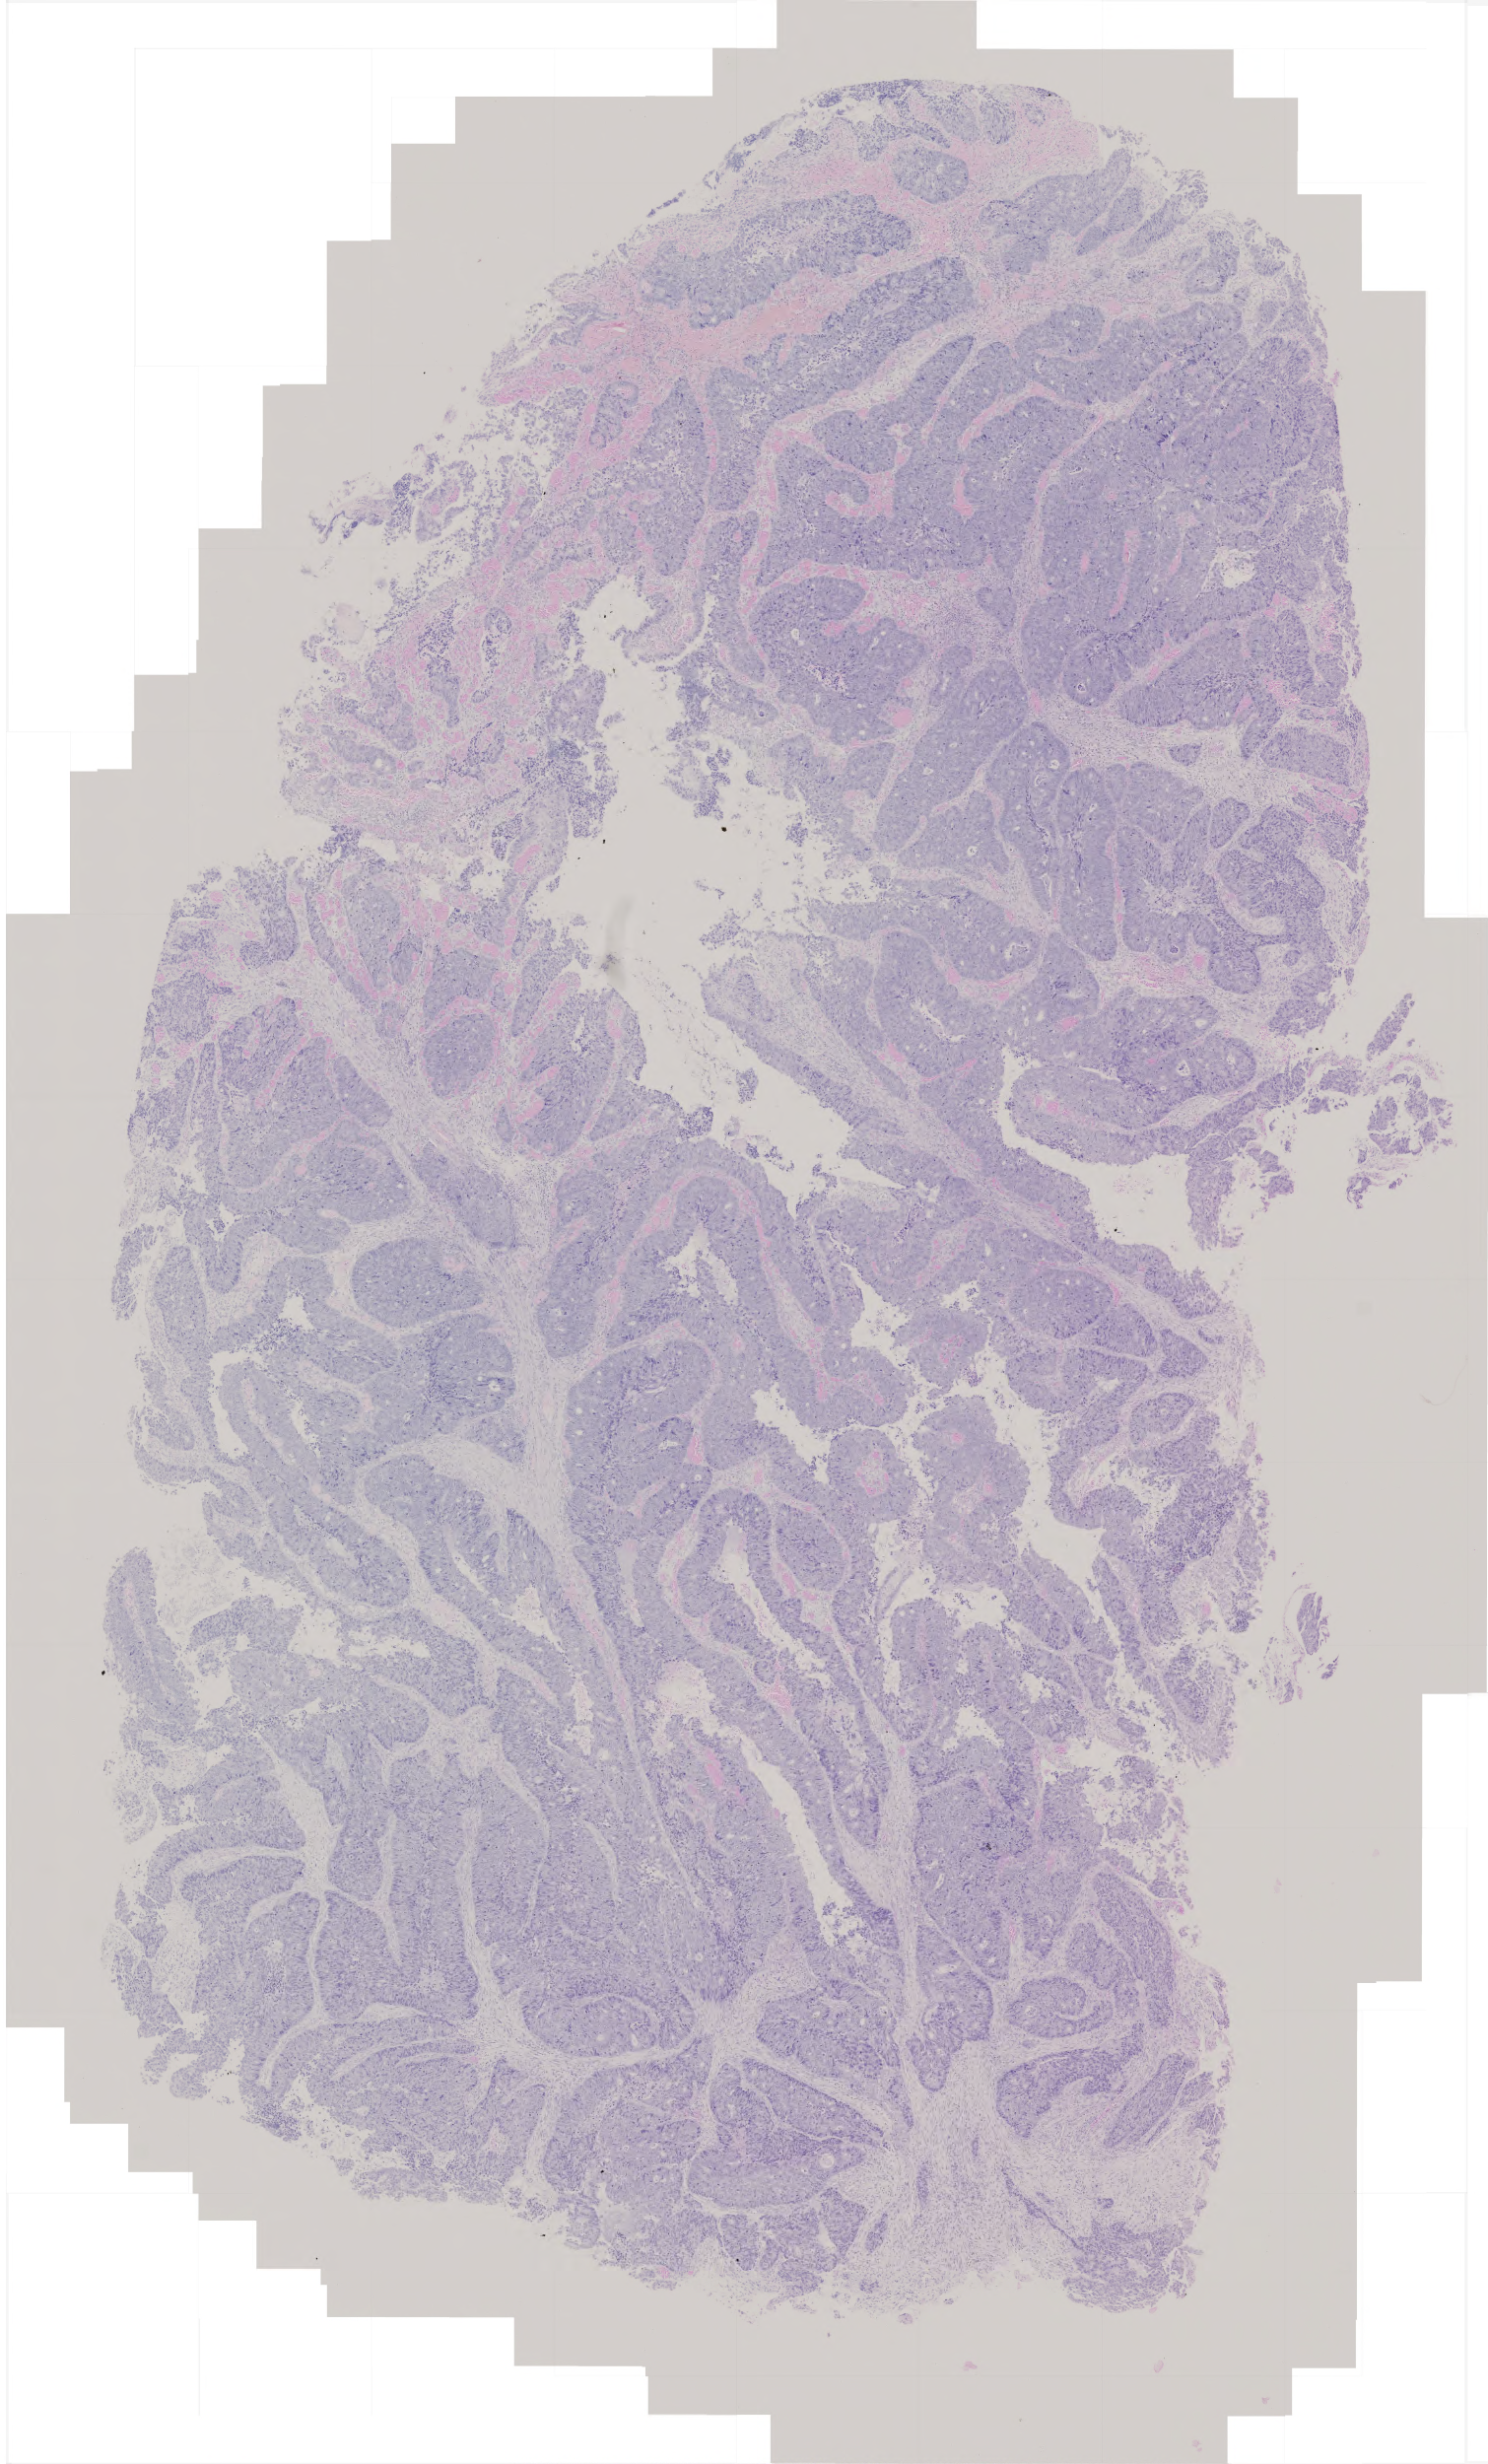
H&E-stained whole-slide image, a low-resolution overview of the entire scanned area, about 3.0 x 5.0 mm; formalin-fixed paraffin-embedded (FFPE) diagnostic section; rectum, primary tumour sample. Male patient; age at initial diagnosis 65 years.
Diagnosis: Adenocarcinoma, NOS. TNM: T3 N1 M1. AJCC pathologic stage: IV (5th edition). Lymph nodes positive (case pathology): 3 of 34 examined.